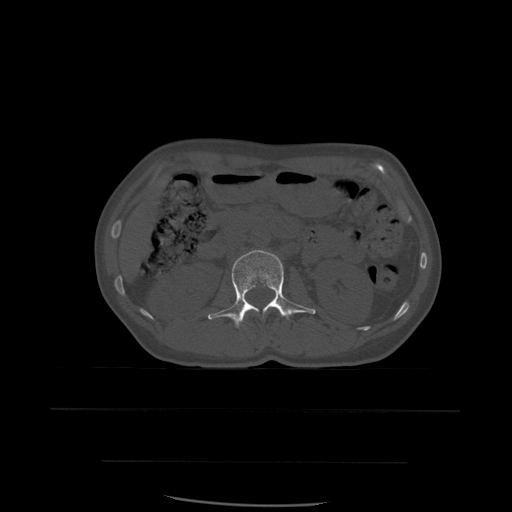
CT including the spine, one axial slice. Position 228 of 574 along the scan axis. Bone window (W 1800 / L 400 HU). 512 × 512 image matrix, field of view 392 × 392 mm. Patient age 48 years. From the clinical record (not read from this slice): primary cancer: lung.
Outlined on this slice (semi-automatically segmented with operator editing):
- L1 vertebra: bounding box <245,313,248,319> (left, top, right, bottom; pixels)
- L2 vertebra: <208,250,316,329>